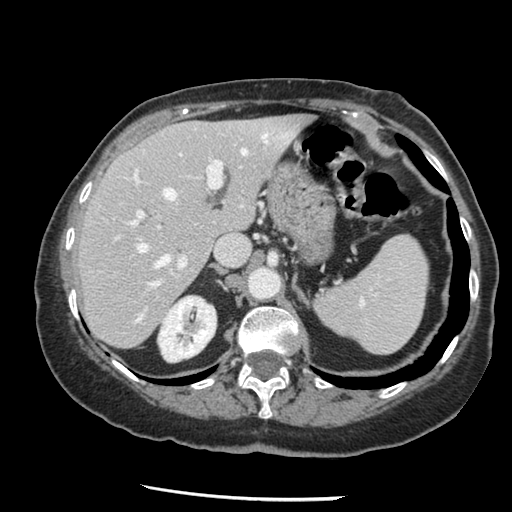
Contrast-enhanced abdominal CT, one axial slice; slice 91 of 148 in the series (ordered by position); reconstruction kernel STANDARD; soft-tissue window (W 400 / L 40 HU); 2.5 mm slice thickness; 512 × 512 image matrix, field of view 330 × 330 mm. Female patient, age 85 years. Case-level facts recorded for this patient, not image findings: diagnosis: colorectal cancer liver metastases, imaged before liver resection; multiple liver metastases: no; largest metastasis: 0.9 cm.
Annotated regions visible in this slice (expert manual segmentation):
- hepatic veins: bounding box <137,134,293,321> (left, top, right, bottom; pixels)
- liver: <80,117,310,348>
- planned liver remnant (the part of the liver to remain after resection): <80,117,310,348>
- portal vein (with intrahepatic branches): <116,157,223,287>